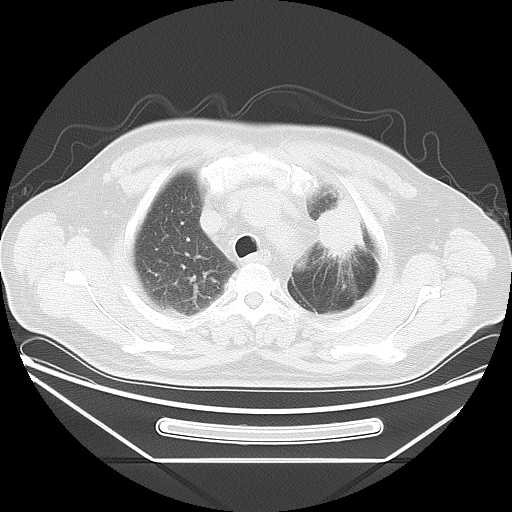
Chest CT, one axial slice. Position 32 of 37 along the scan axis. Reconstruction kernel LUNG. 120 kVp. Lung window (W 1500 / L -600 HU). 5 mm slice thickness. 512 × 512 image matrix. Male patient, age 61 years. Case-level facts recorded for this patient, not image findings: clinical TNM (as recorded): T2a N0 M0; histopathological grade: G3.
Annotated regions visible in this slice (bounding box drawn by a radiologist):
- lung tumour (recorded histology: small cell carcinoma): bounding box <307,186,372,268> (left, top, right, bottom; pixels)